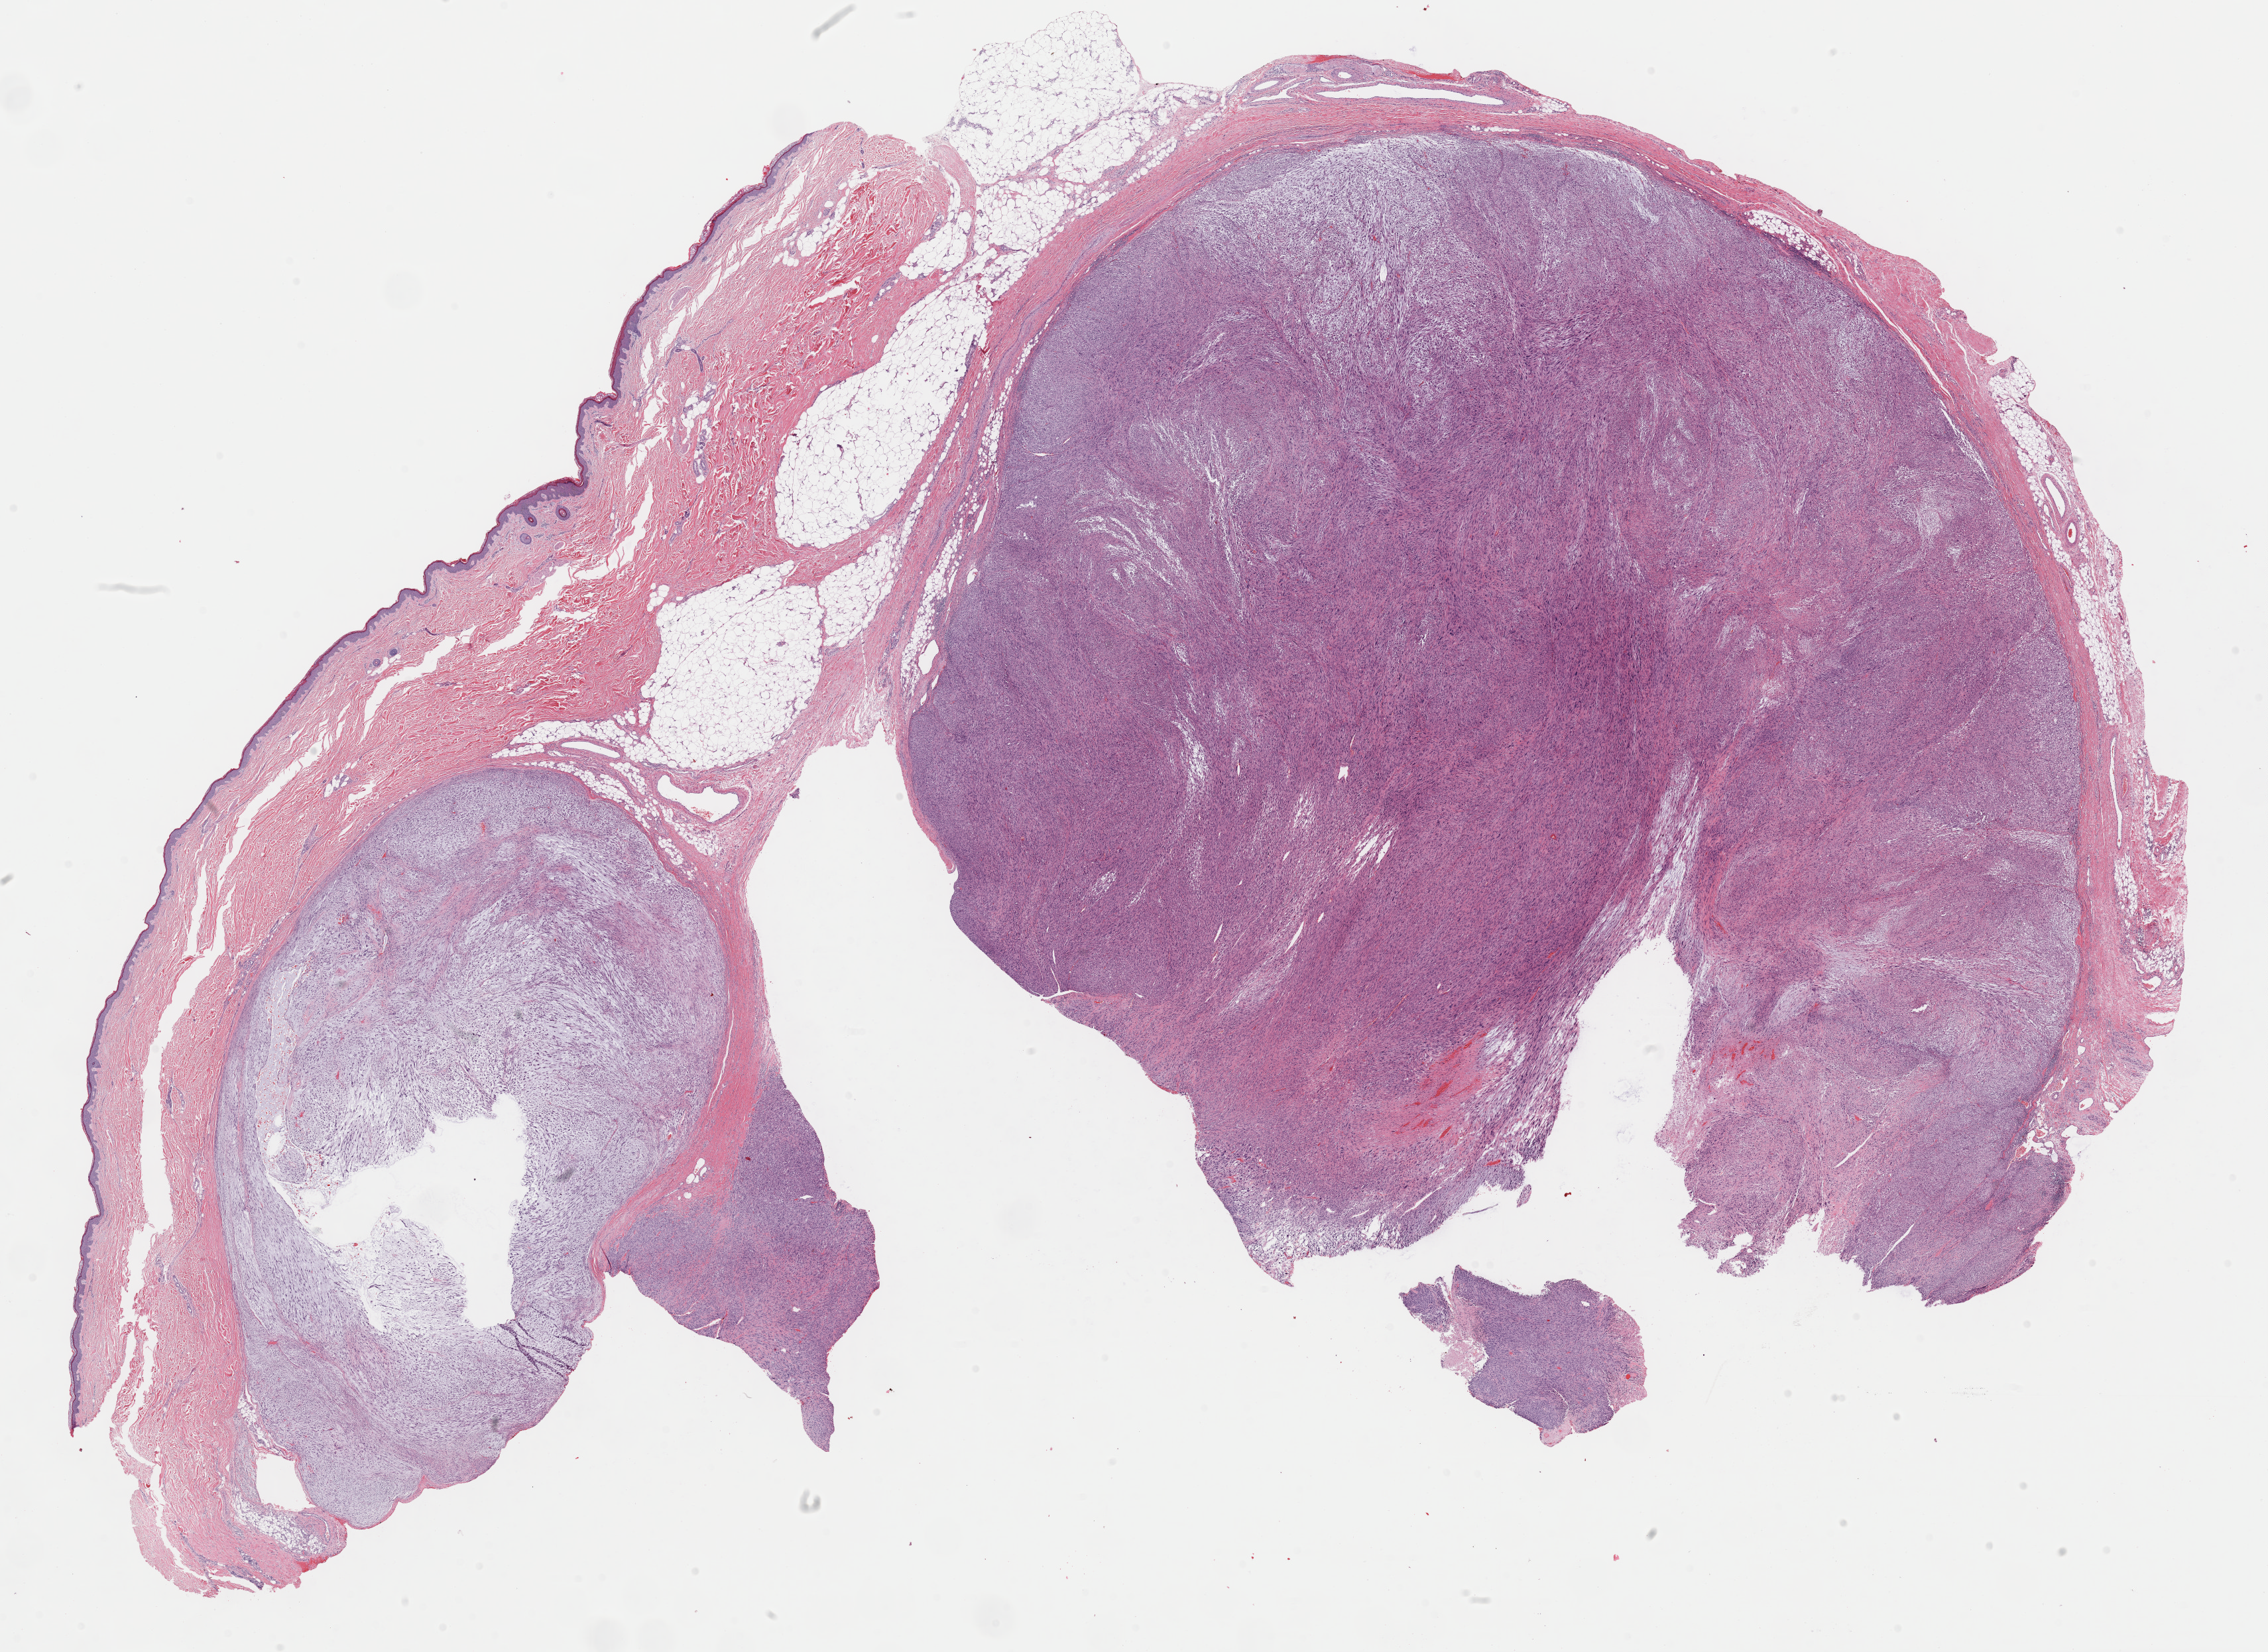
Digitized Hematoxylin and eosin (H&E) stained tissue section (whole slide) — low-resolution overview of the scanned area, about 27.0 x 19.7 mm (slide scanned at 40x); formalin-fixed paraffin-embedded (FFPE) diagnostic section; sample: primary tumour, connective, subcutaneous and other soft tissues. Female patient; age at initial diagnosis 63 years.
• pathologic diagnosis: Leiomyosarcoma, NOS (connective, subcutaneous and other soft tissues, NOS)